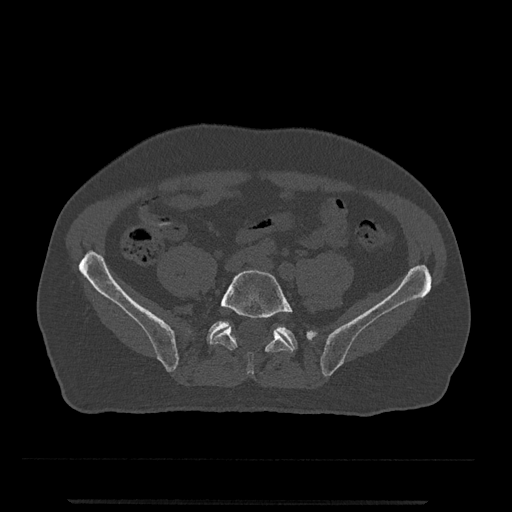
CT including the spine, one axial slice. Position 60 of 797 along the scan axis. Reconstruction kernel Br40s/3. 120 kVp. Bone window (W 1800 / L 400 HU). 0.5 mm slice thickness. 512 × 512 image matrix, field of view 419 × 419 mm. Patient: male, 63 years. Case-level facts recorded for this patient, not image findings: primary cancer: prostate.
Annotated regions visible in this slice (semi-automatically segmented with operator editing):
- L5 vertebra: box from (x=211, y=269) to (x=294, y=375) px